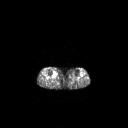
FDG PET of an extremity soft-tissue mass (from a PET/CT study), one axial slice. Slice 151 of 267 in the series (ordered by position). 3.27 mm slice thickness. 128 × 128 image matrix. Patient: female, 65 years. Case-level facts recorded for this patient, not image findings: histological type: undifferentiated – high grade; grade: high; site of the primary tumour: right thigh.
Structures marked on this image (expert contour drawn on MRI and transferred to this co-registered scan by the dataset authors):
- gross tumour volume (mass): bounding box (x1, y1, x2, y2) in pixels: (53, 72, 57, 77)